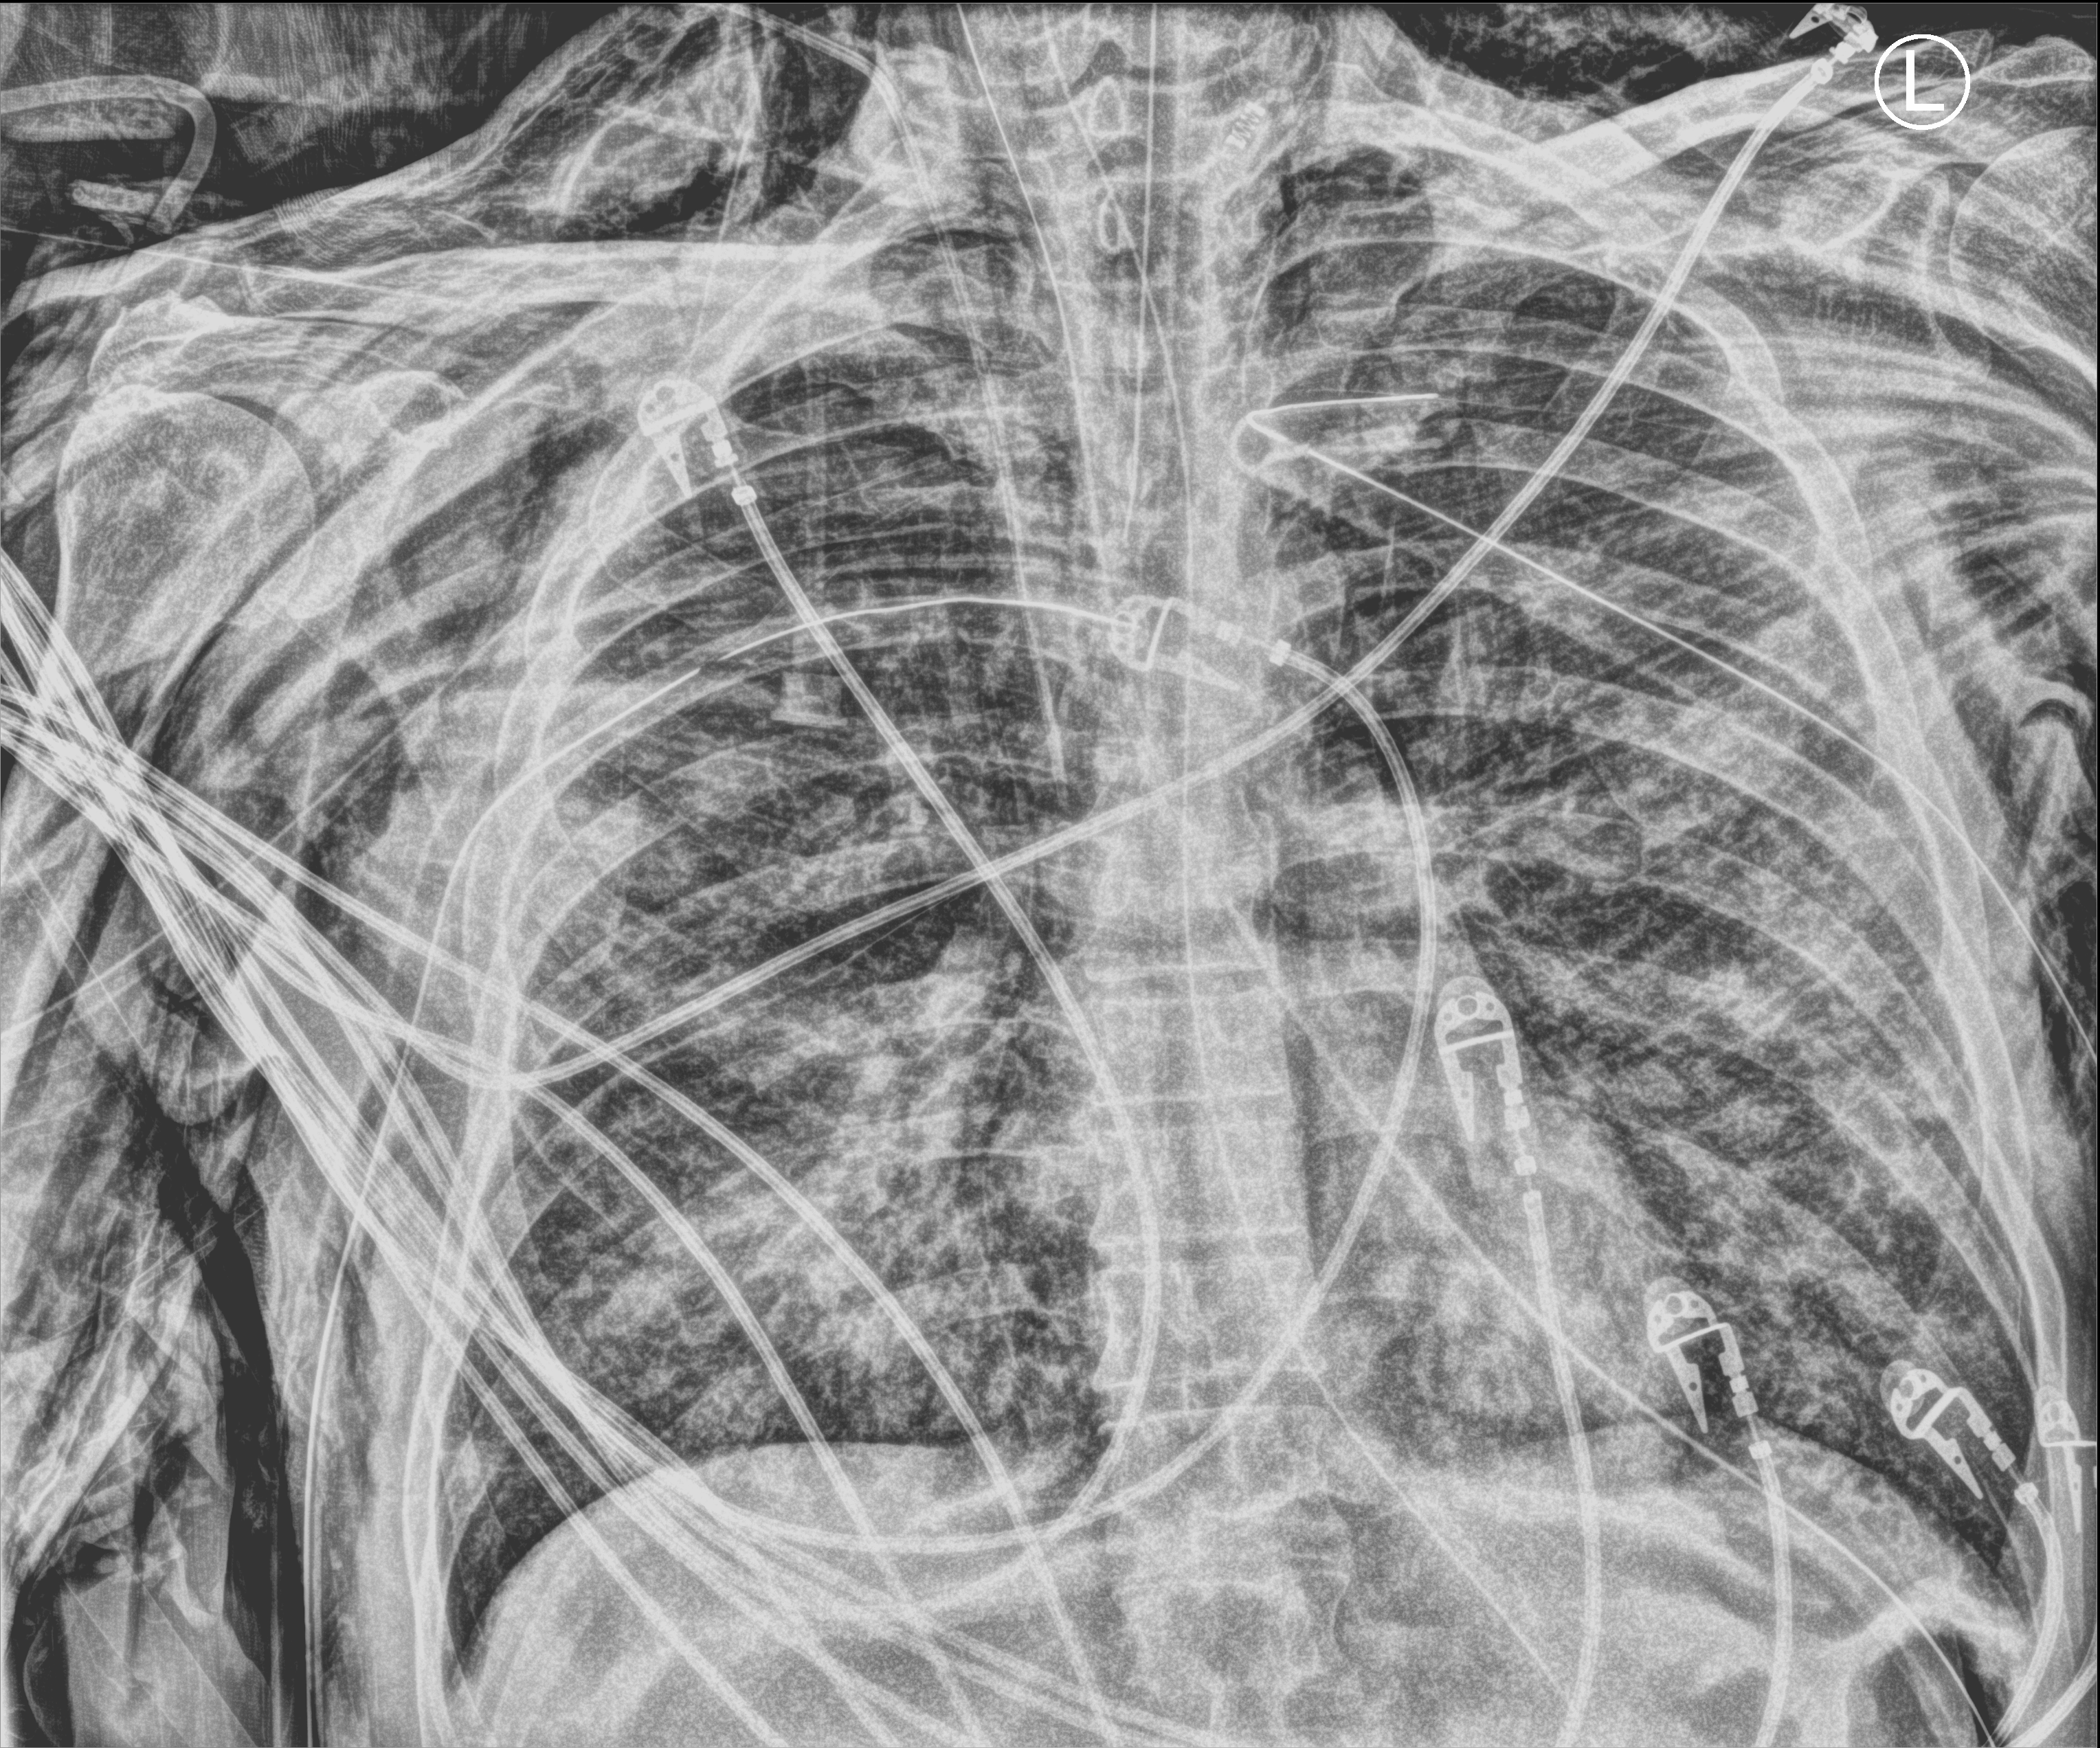
Chest X-ray (portable). Male patient hospitalised with COVID-19, age 18–59 years.
From the hospital-stay record, not from the radiograph (when in the stay this image was taken is not recorded): hypertension (admission record): yes; smoking status (admission record): never.